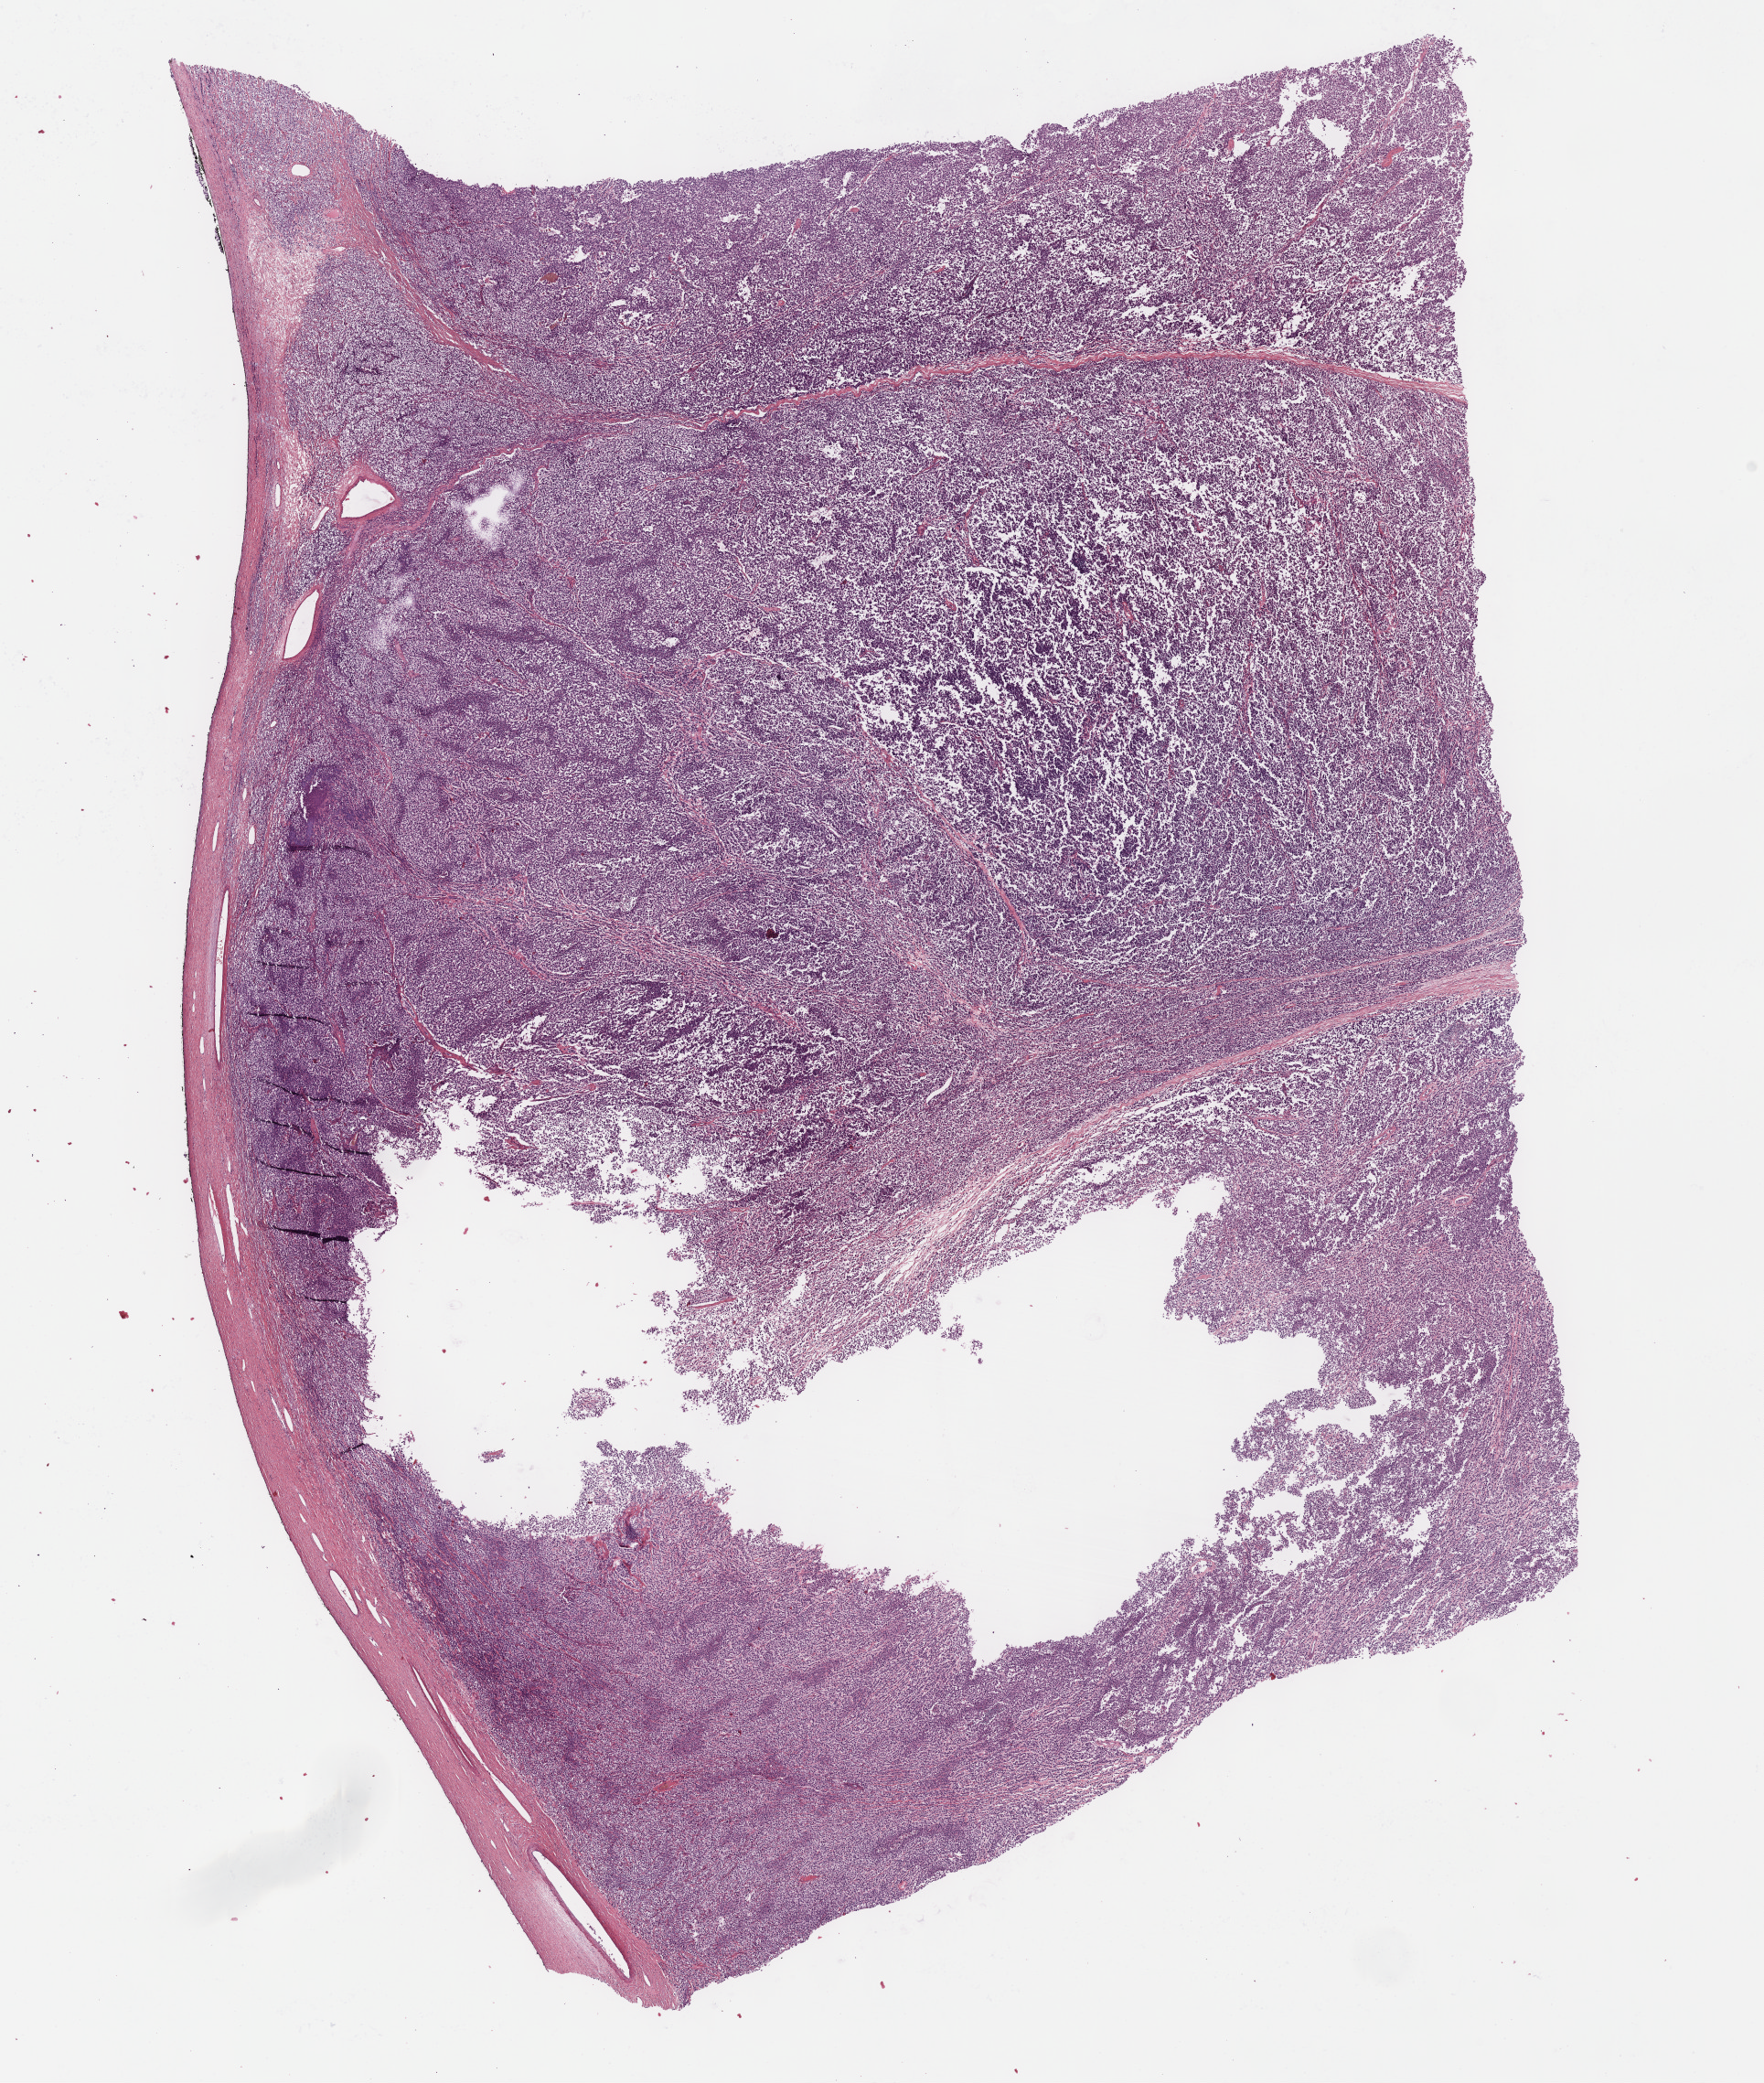
Digitized H&E tissue section (whole slide) — shown as a low-resolution overview of the whole scanned area (about 15.6 x 18.4 mm, from a 40x scan). FFPE section. Testis, primary tumour sample. Male, age 21 years at initial diagnosis.
AJCC pathologic stage: IB (6th edition). Pathologic diagnosis: Seminoma, NOS.